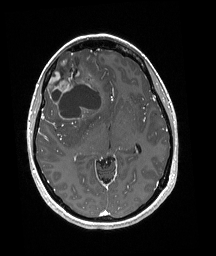
Brain MRI from a brain-tumour surgery series, one axial slice. Slice 106 of 192 in the series (ordered by position). T1-weighted post-contrast. 1 mm slice thickness. 216 × 256 image matrix, field of view 211 × 250 mm. Case-level facts recorded for this patient, not image findings: histopathology: Oligodendroglioma; WHO grade: 3; IDH mutation: yes.
Outlined on this slice (outlined manually by an expert reader):
- tumour: bounding box <48,51,101,121> (left, top, right, bottom; pixels)